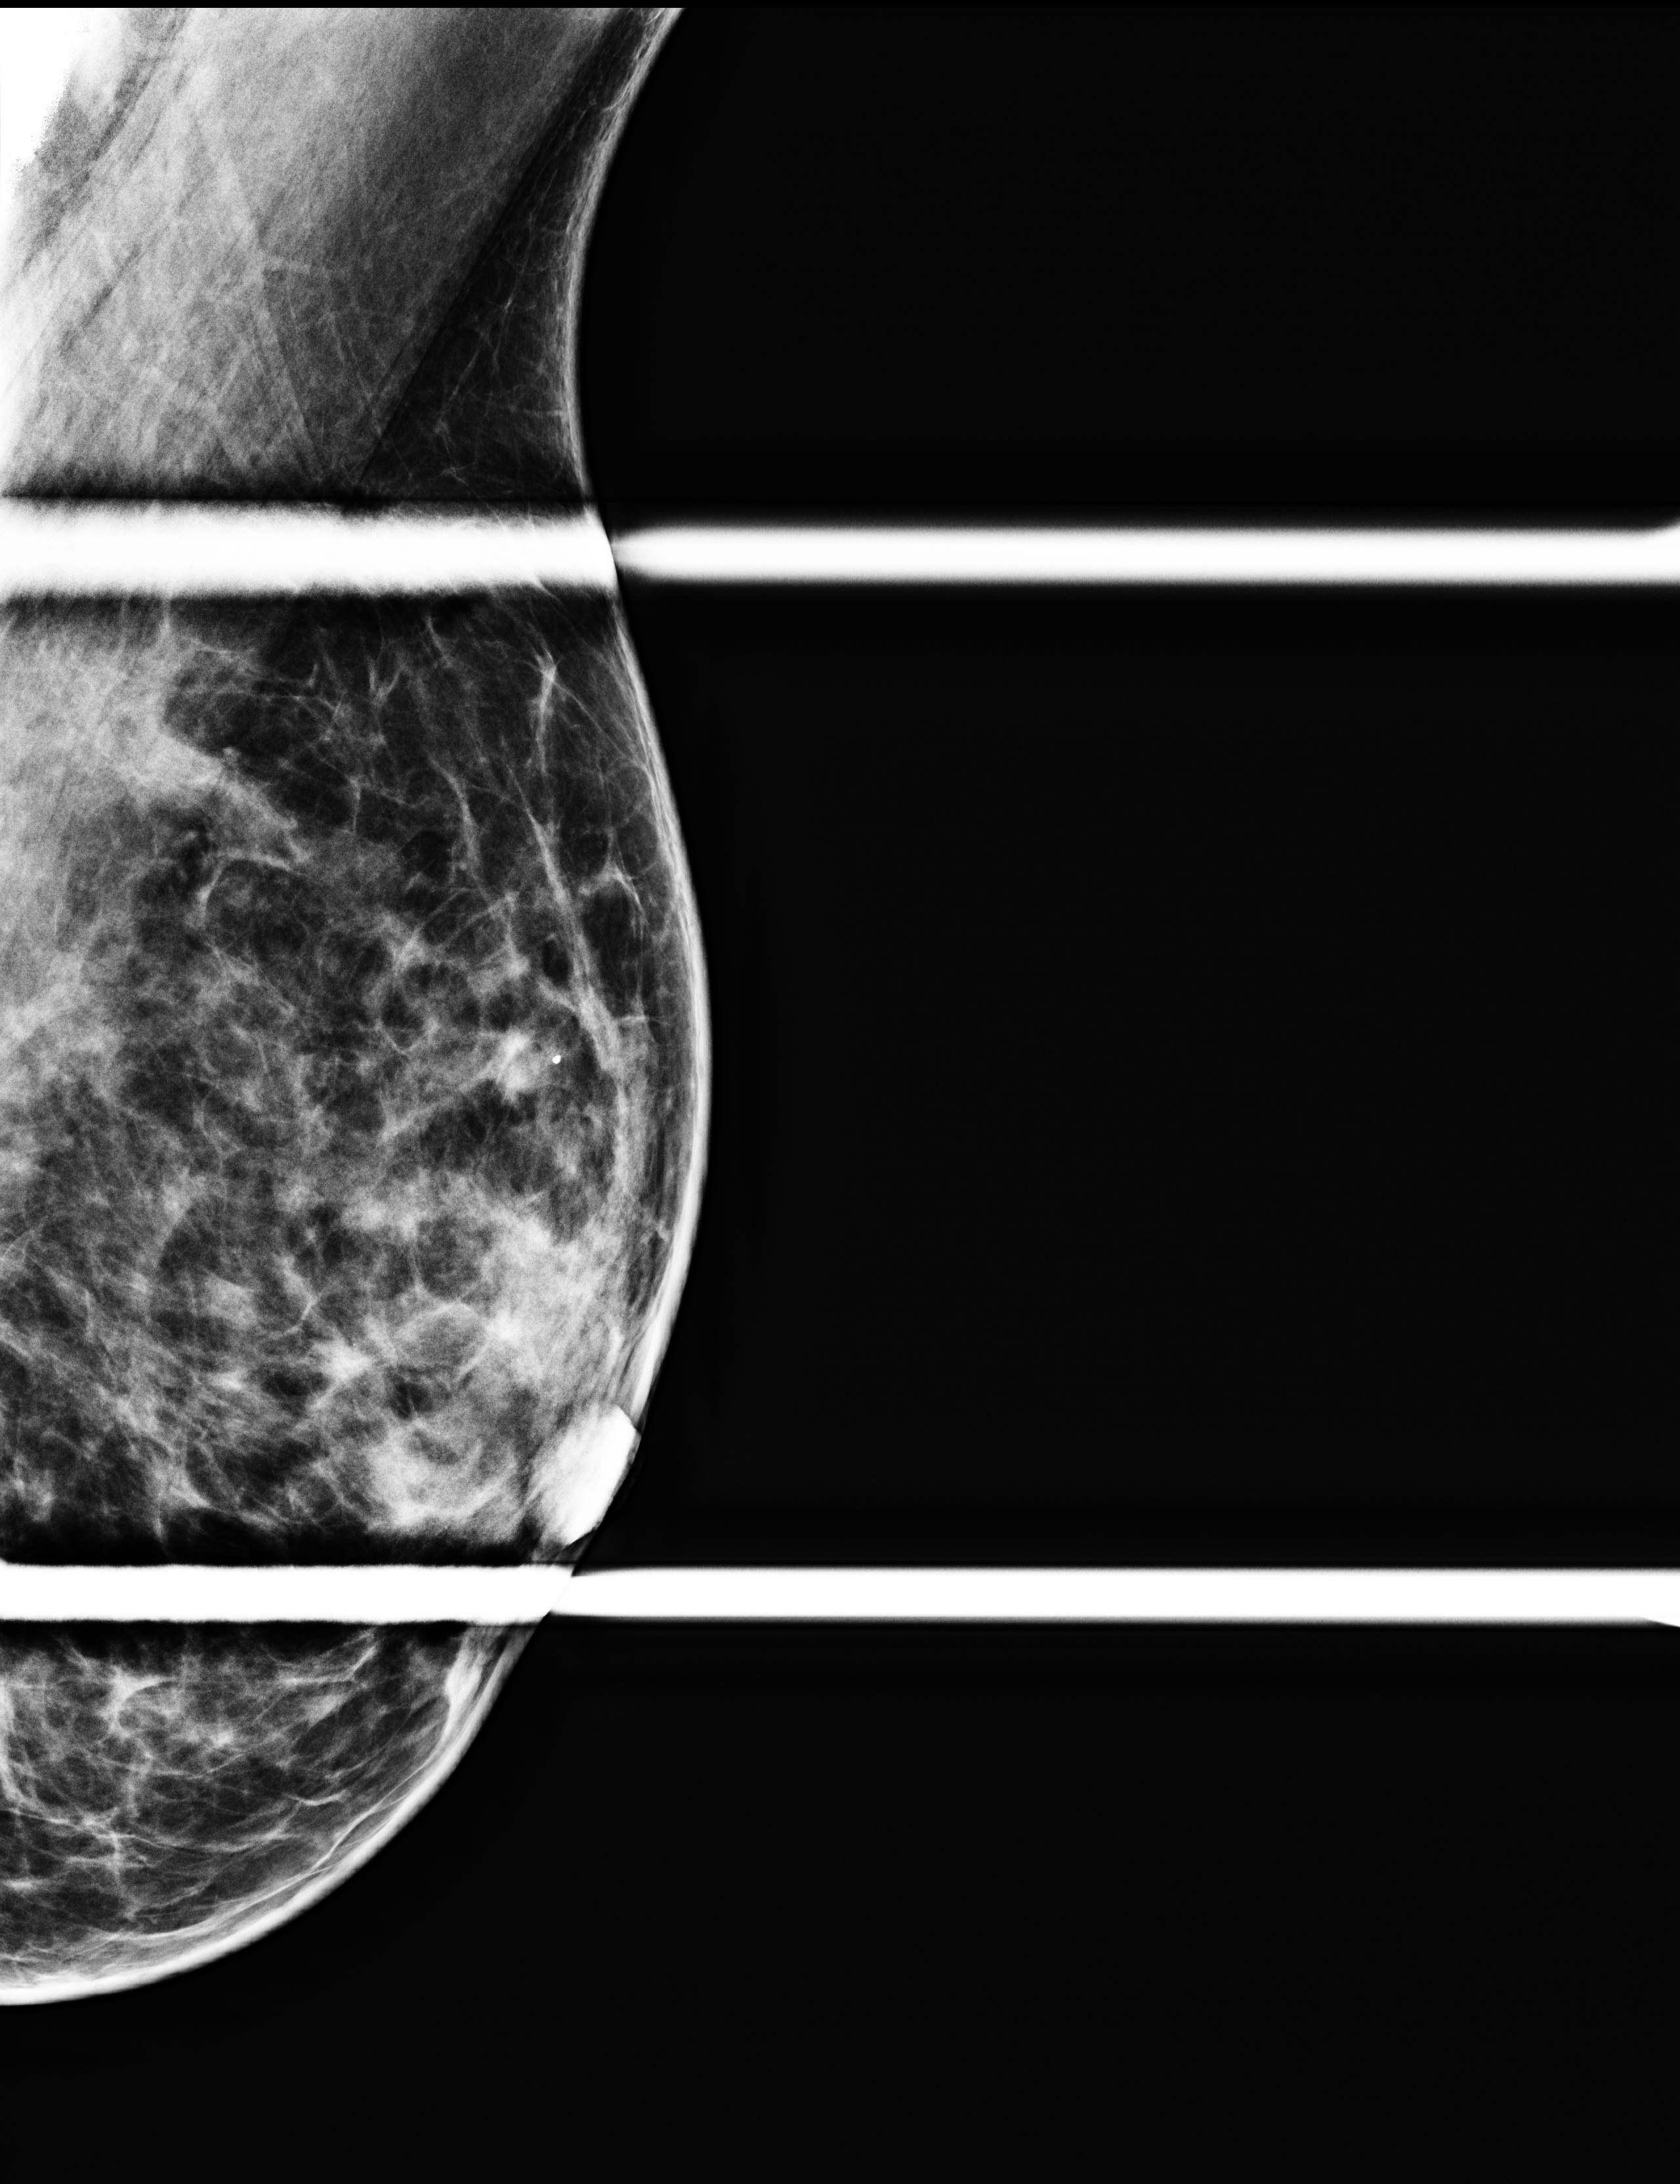
Digital mammogram (FFDM); left breast; medio-lateral oblique projection (spot compression); screening examination. Patient: female, 43 years.
- breast density at the screening exam (both breasts): heterogeneously dense (BI-RADS density category c)
- final BI-RADS assessment for this screening round (tomosynthesis exam, both breasts): category 2
- recall: no recall after this screen